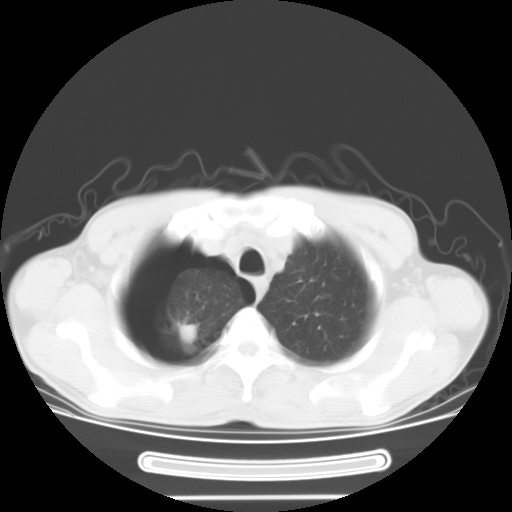
Chest CT, one axial slice. Slice 29 of 34 in the series (ordered by position). Reconstruction kernel STANDARD. Lung window (W 1500 / L -600 HU). 10 mm slice thickness. 512 × 512 image matrix, field of view 375 × 375 mm. Male patient. Case-level facts recorded for this patient, not image findings: clinical TNM (as recorded): T1c N0 M0.
Outlined on this slice (bounding box drawn by a radiologist):
- lung tumour (recorded histology: adenocarcinoma): bounding box <179,313,198,345> (left, top, right, bottom; pixels)